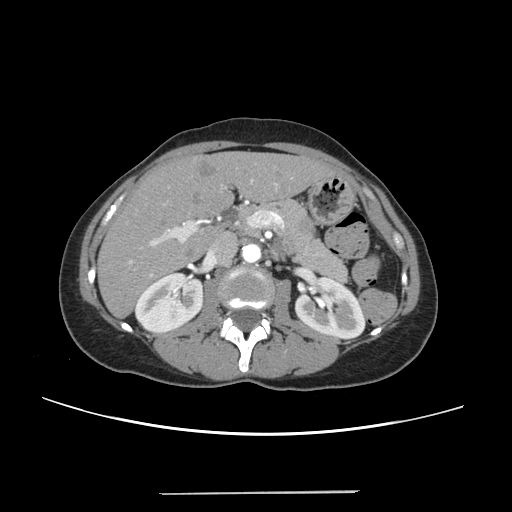
Contrast-enhanced abdominal CT, one axial slice; slice 125 of 240 in the series (ordered by position); intravenous contrast given; soft-tissue window (W 400 / L 40 HU); 1.25 mm slice thickness; 512 × 512 image matrix. Female patient, age 60 years. Case-level facts recorded for this patient, not image findings: diagnosis: colorectal cancer liver metastases, imaged before liver resection; multiple liver metastases: no; largest metastasis: 1.5 cm.
Annotated regions visible in this slice (expert manual segmentation):
- liver: bounding box (x1, y1, x2, y2) in pixels: (99, 152, 330, 316)
- planned liver remnant (the part of the liver to remain after resection): (99, 153, 330, 316)
- portal vein (with intrahepatic branches): (129, 179, 278, 276)
- liver metastasis: (199, 161, 218, 178)